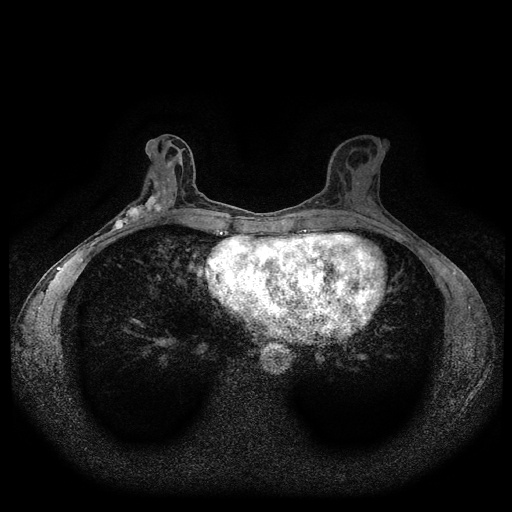
Breast MRI (dynamic contrast-enhanced, multi-phase), one axial slice. Position 46 of 116 along the scan axis. Dynamic contrast-enhanced series, time point 2 of 5 at this slice position (early post-contrast). 1.5 T. TE 2.6 ms, TR 5.3 ms. 2 mm slice thickness. 512 × 512 image matrix, field of view 350 × 350 mm. Female patient, age 50 years.
Annotated regions visible in this slice (semi-automatic segmentation, software-assisted and operator-edited):
- breast lesion (labelled 'tumour' in the annotation; benign lesions carry a separate 'benign' label): box from (x=111, y=175) to (x=169, y=232) px